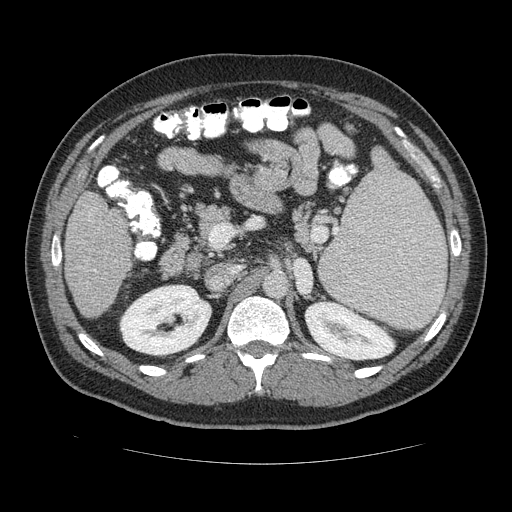
Contrast-enhanced abdominal CT (liver protocol), one axial slice; slice 62 of 113 in the series (ordered by position); soft-tissue window (W 400 / L 40 HU); 2.5 mm slice thickness; 512 × 512 image matrix. From the clinical record (not read from this slice): diagnosis: hepatocellular carcinoma (patient treated with transarterial chemoembolisation; whether this scan precedes or follows treatment is not stated here); TNM stage (as recorded): Stage-II; Child-Pugh class: B; tumour differentiation: moderately differentiated; tumour size: 4.8 cm.
Structures marked on this image (semi-automatic segmentation, software-assisted and operator-edited):
- liver parenchyma outside the tumour (the mass and vessels are separate outlines, so this box may not span the whole liver): bounding box [x1, y1, x2, y2] px = [64, 186, 134, 320]
- liver vessels: [87, 217, 95, 272]